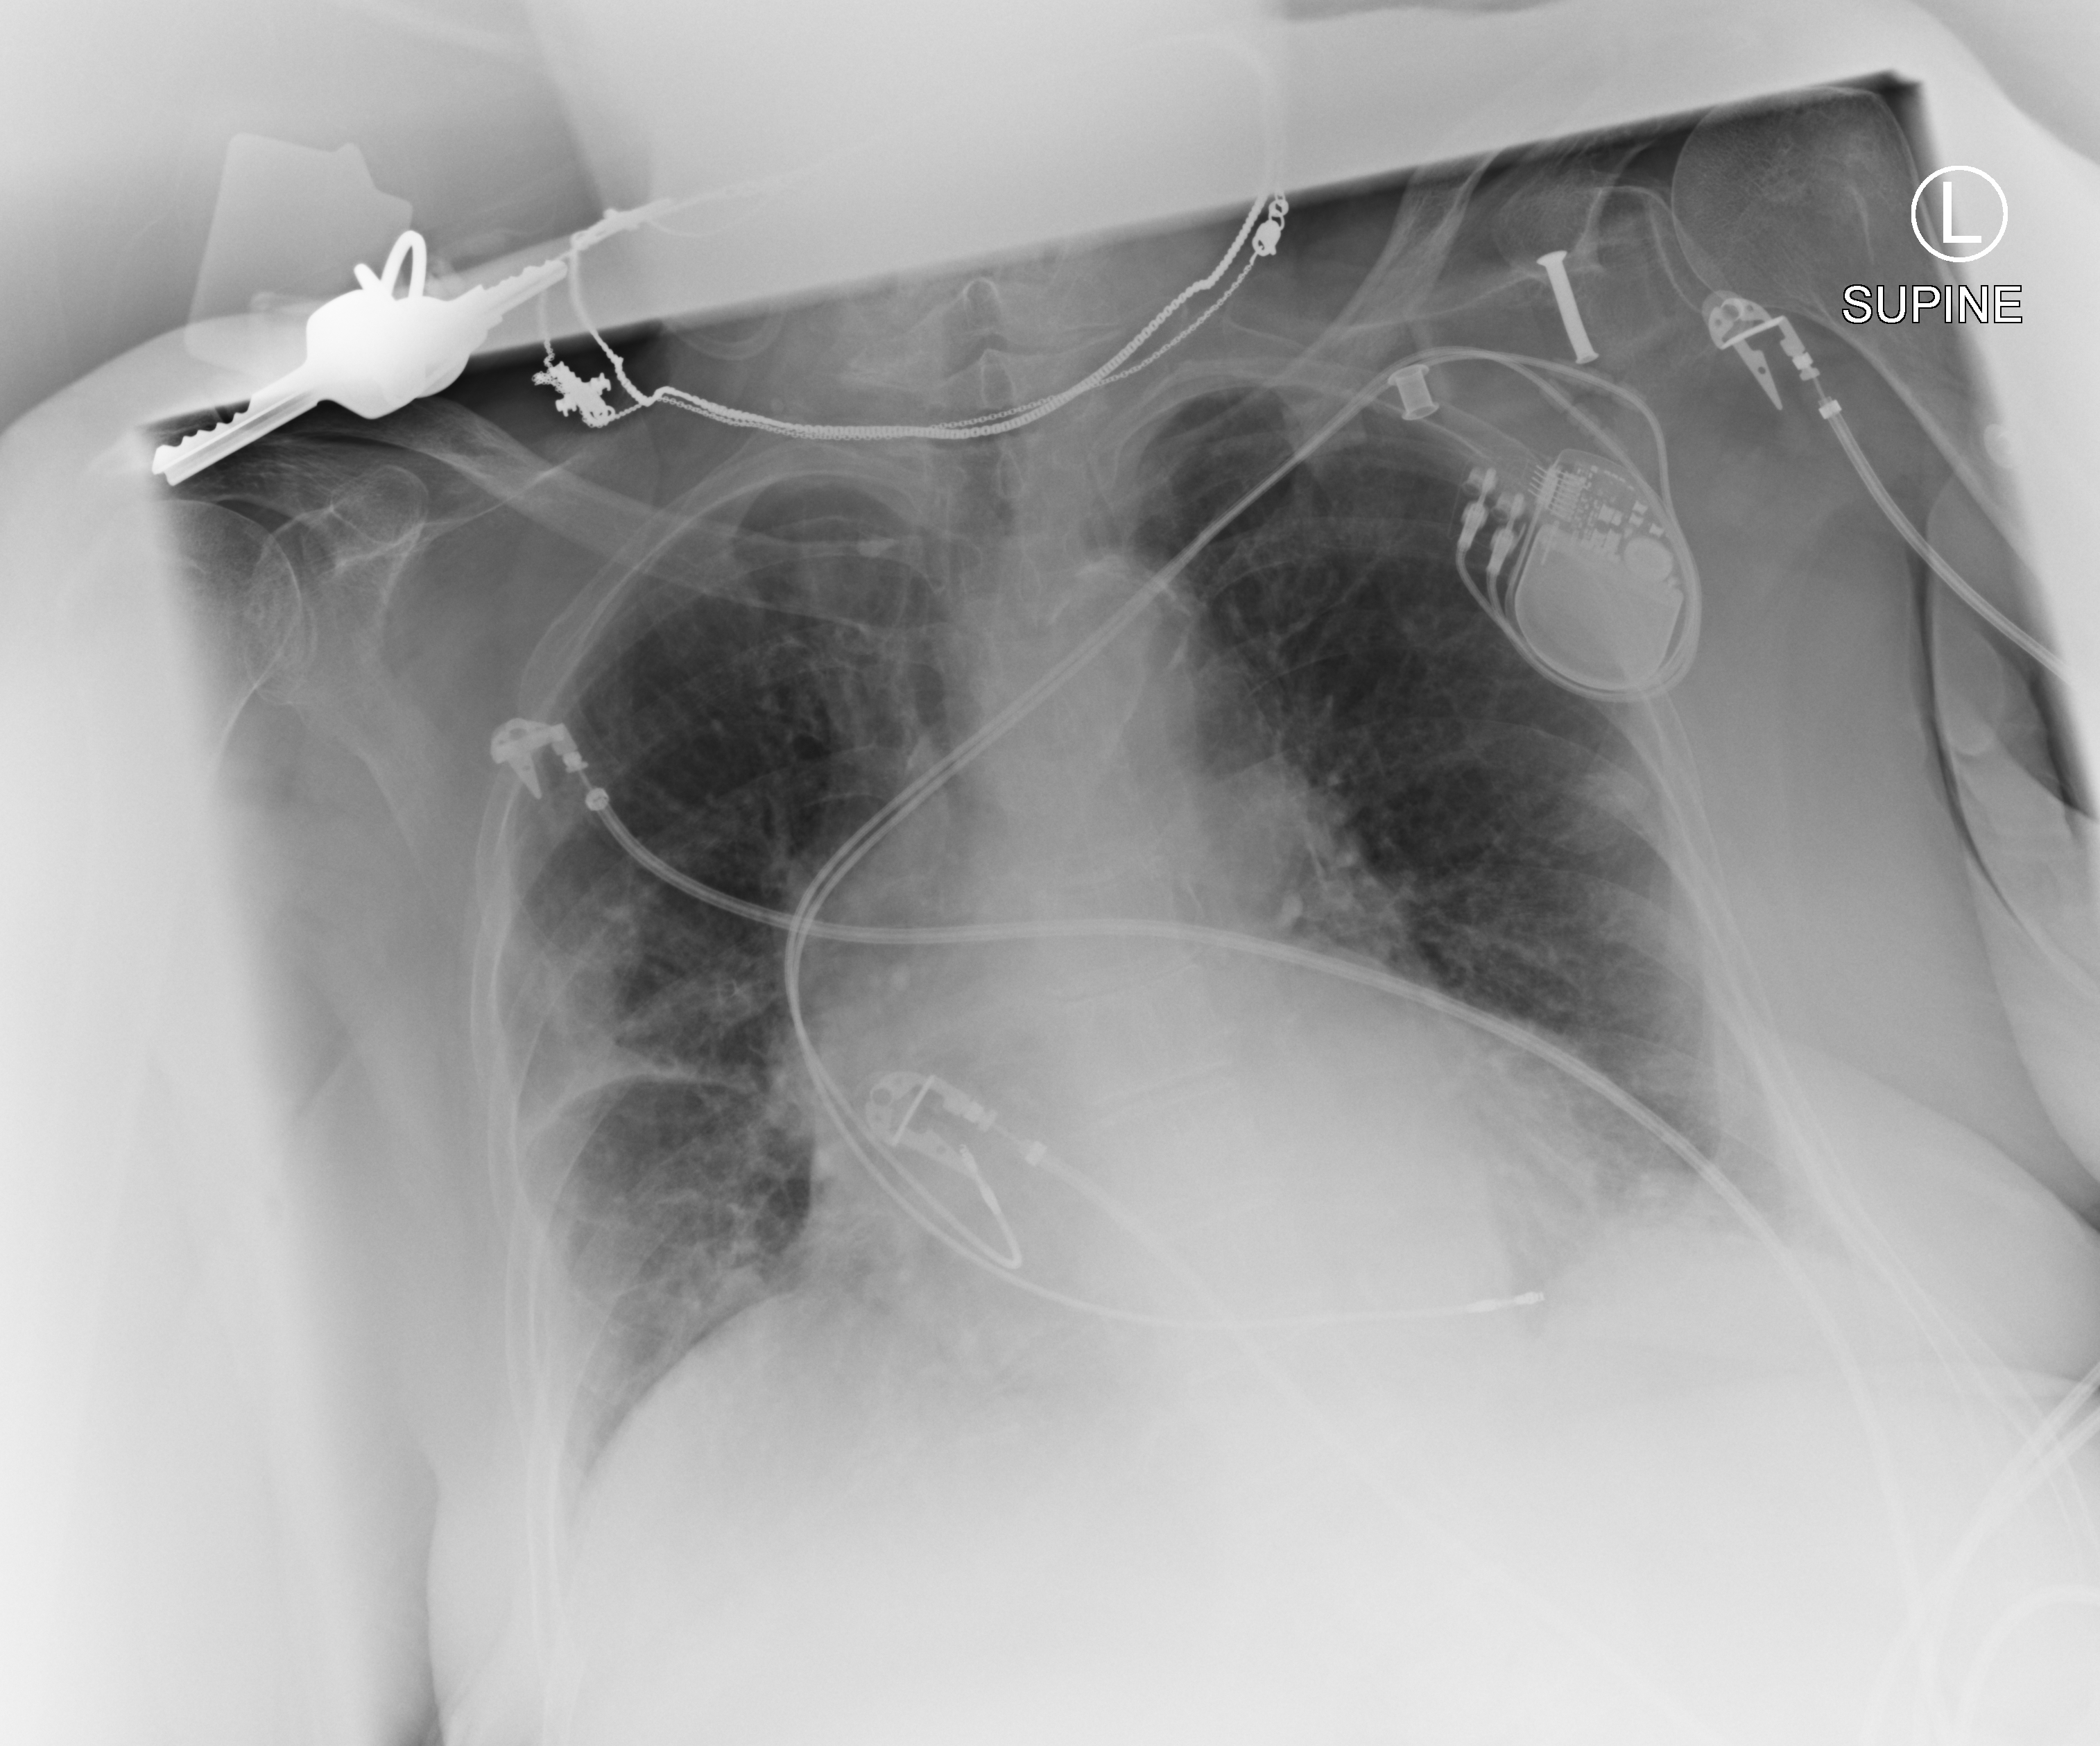
Bedside chest radiograph (computed radiography); anteroposterior (AP) projection. Patient hospitalised with COVID-19; female, aged 75–90 years.
Admission-level facts for this patient (not findings on this image; timing relative to this image not recorded): COPD (admission record): no; smoking status (admission record): never; mechanically ventilated during this hospital stay: no.